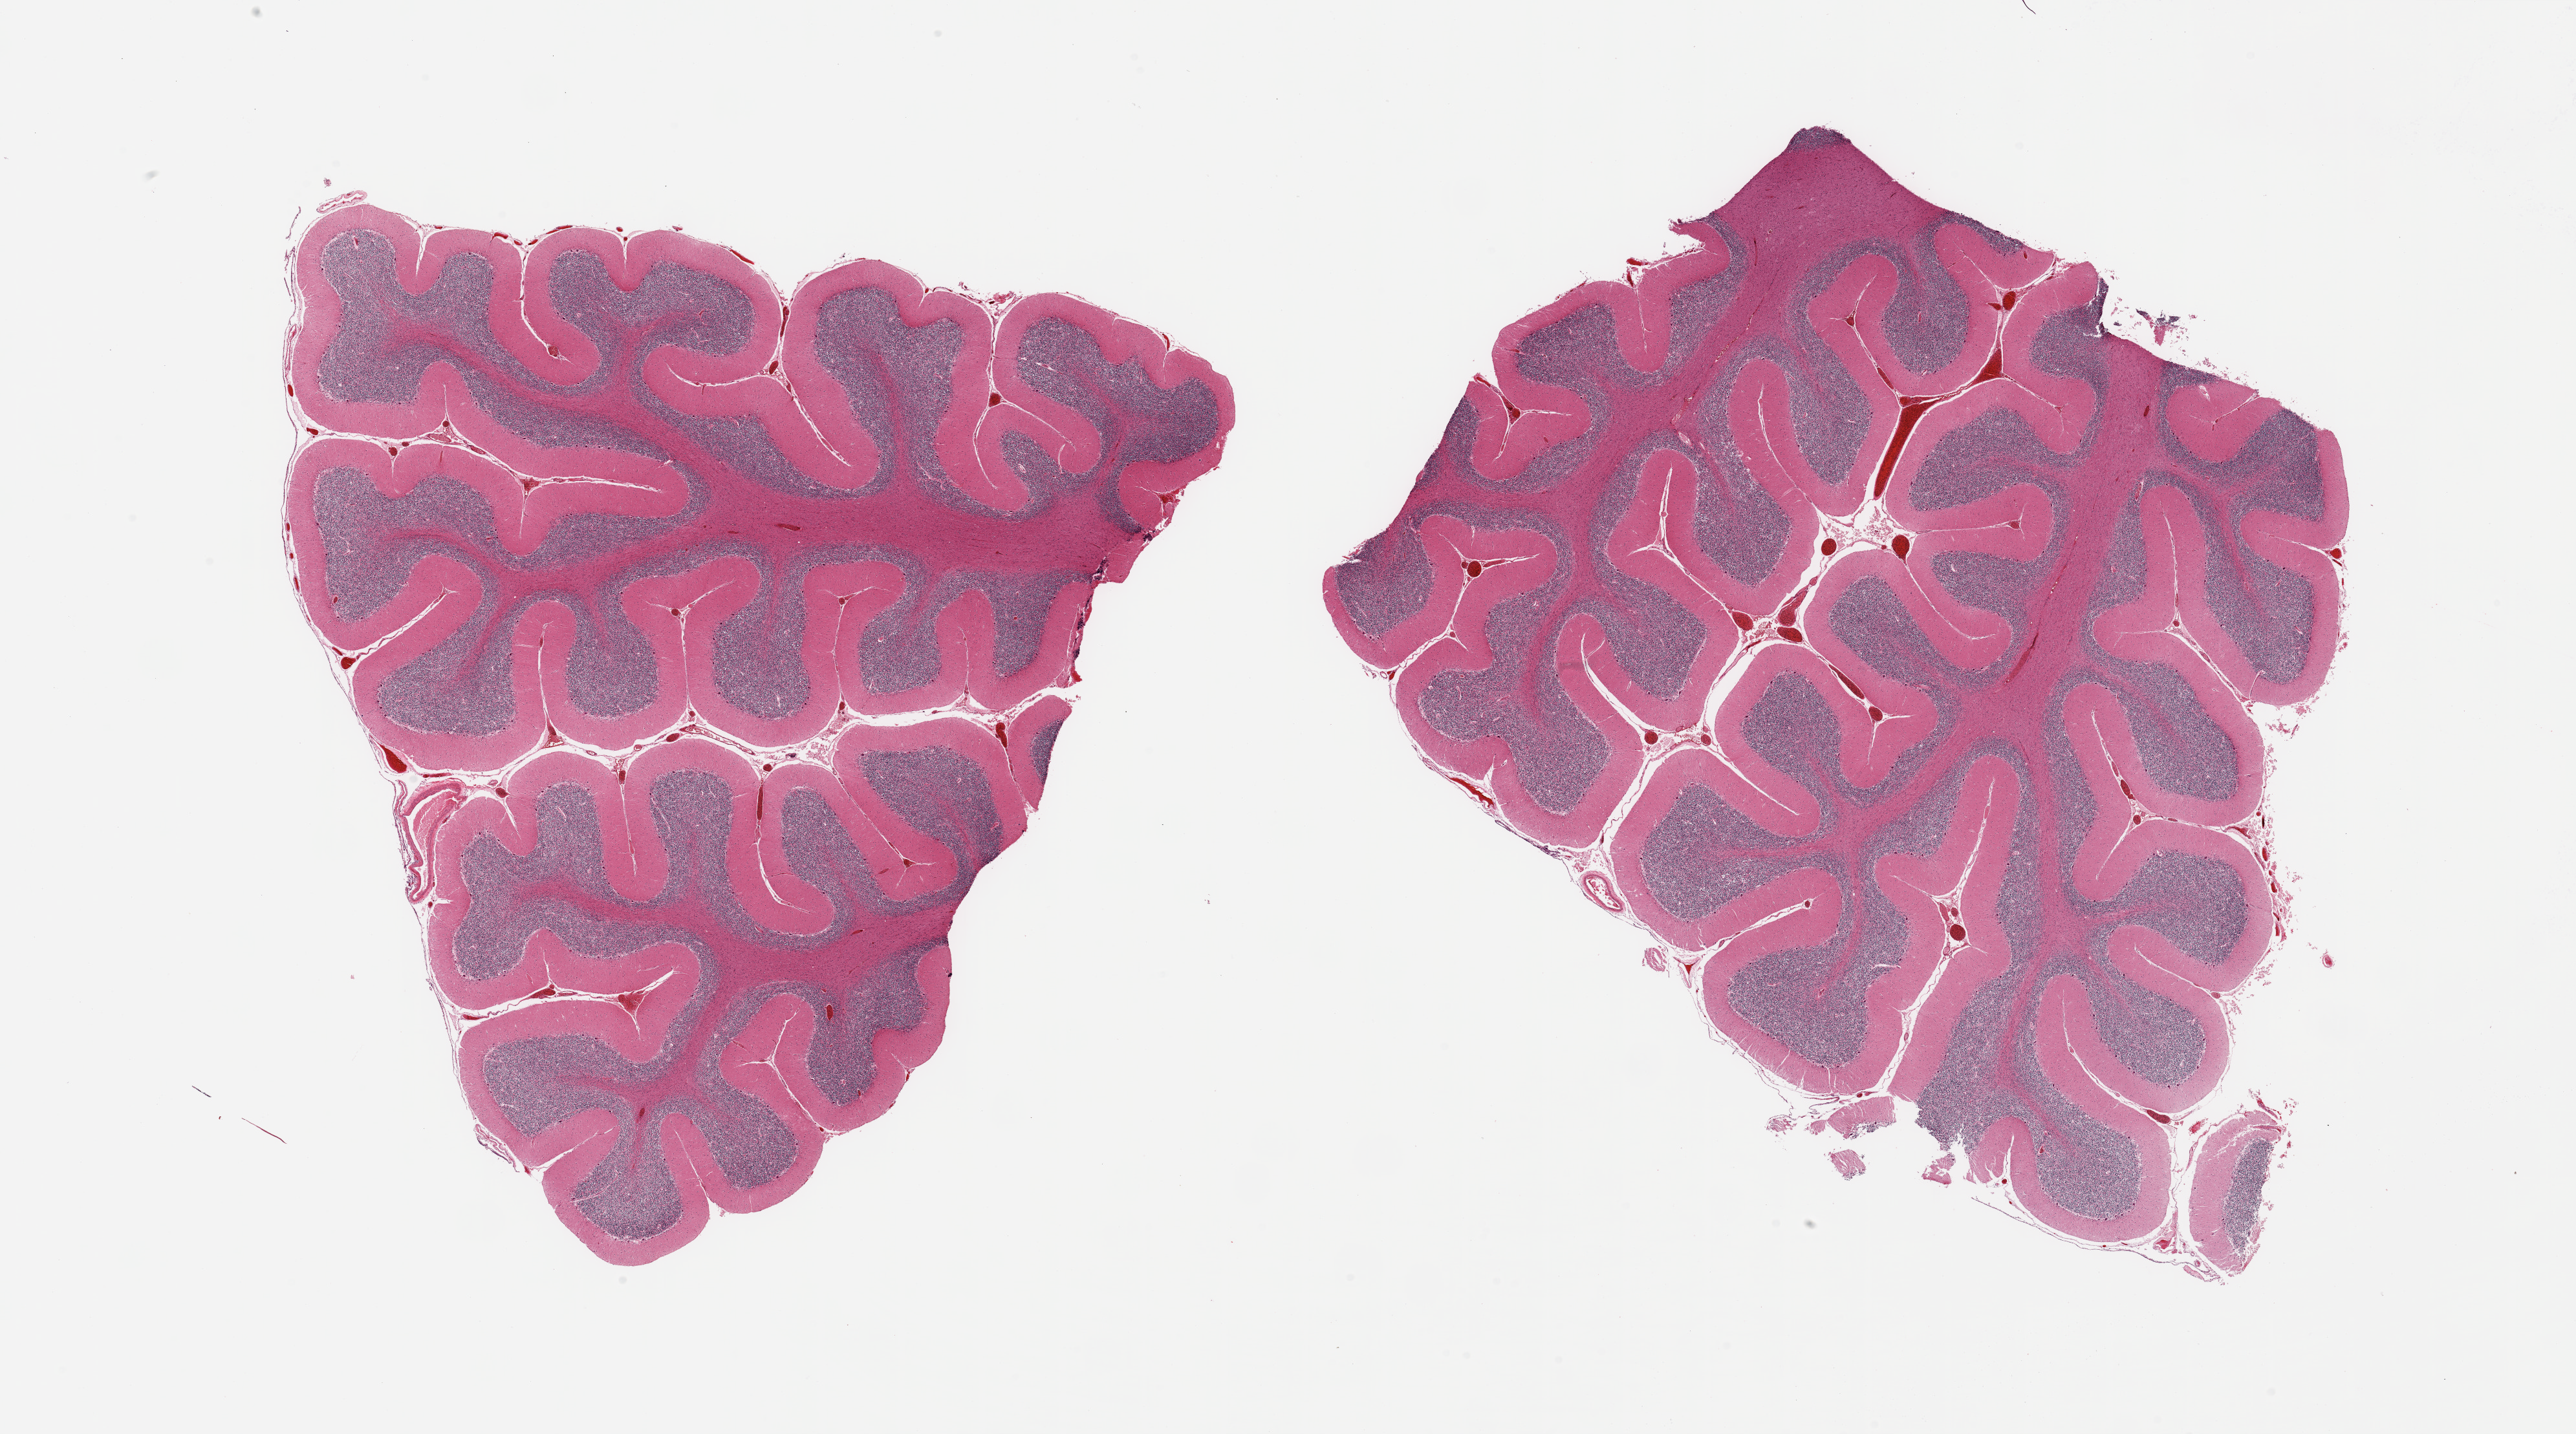
Whole-slide image, hematoxylin and eosin (H&E) stain, whole scanned area (about 31.5 x 17.5 mm, from a 20x scan) shown as a low-resolution overview. PAXgene-fixed, paraffin-embedded tissue. Target tissue: cerebellum. Donor tissue sample. Donor: male.
* reviewer comment on this tissue sample: 2 pieces, no abnormalities